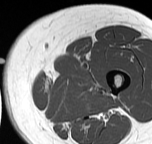
MRI of an extremity soft-tissue mass, one axial slice; position 10 of 57 along the scan axis; MR volume resampled by the dataset authors to the PET/CT grid (not the native acquisition matrix); 3.27 mm slice thickness; 152 × 144 image matrix. Female patient. Case-level facts recorded for this patient, not image findings: histological type: pleiomorphic leiomyosarcoma; grade: intermediate; site of the primary tumour: left thigh.
Outlined on this slice (expert contour drawn on MRI and transferred to this co-registered scan by the dataset authors):
- gross tumour volume including surrounding oedema: box from (x=45, y=74) to (x=101, y=95) px